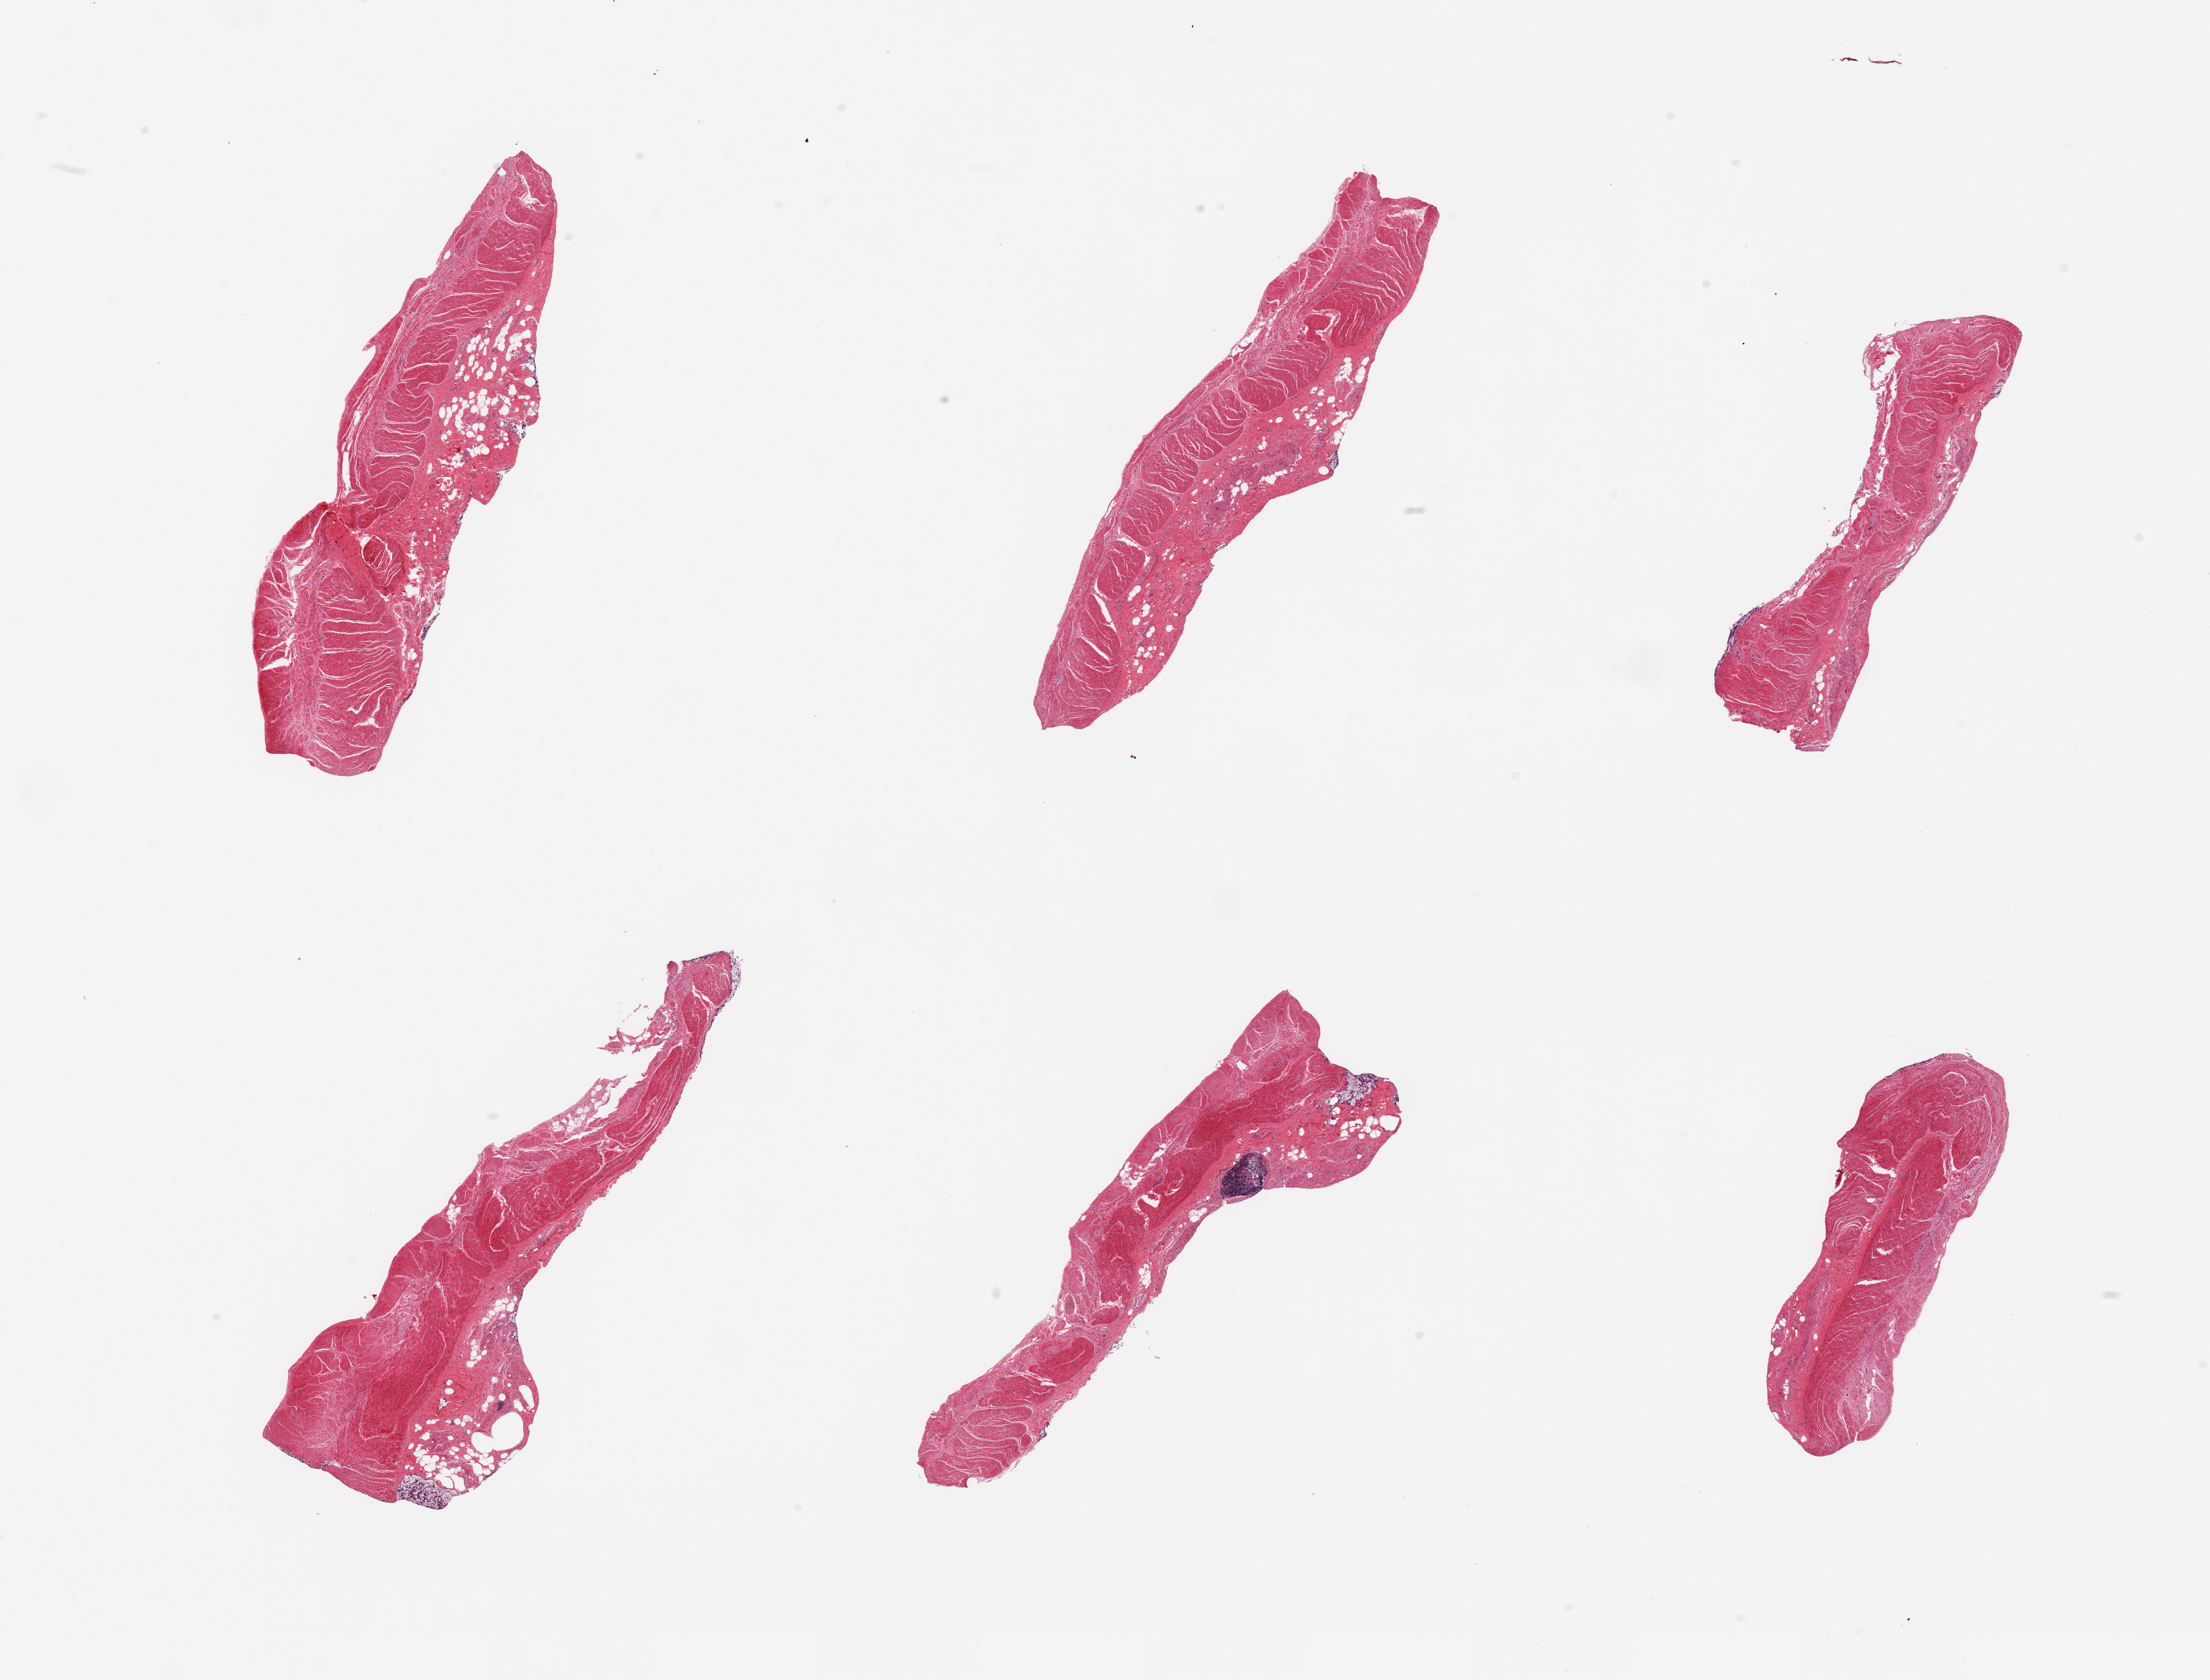
Whole-slide image, haematoxylin and eosin stain, shown as a low-resolution overview of the whole scanned area (about 25.6 x 19.5 mm); PAXgene-fixed paraffin-embedded (PFPE) section; sampled site (target tissue): sigmoid colon; tissue donor sample.
Reviewer comment on this tissue sample: 6 pieces, confirmed target muscularis; inidental lymph node.